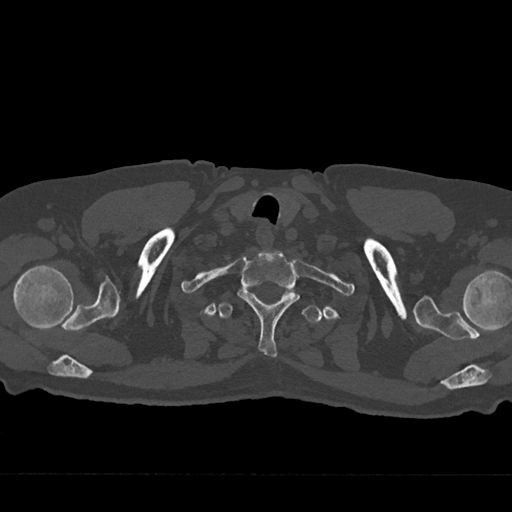
CT including the spine, one axial slice. Slice 651 of 797 in the series (ordered by position). Reconstruction kernel Br40s/3. Bone window (W 1800 / L 400 HU). 0.5 mm slice thickness. 512 × 512 image matrix, field of view 377 × 377 mm. Patient: male, 75 years. Case-level facts recorded for this patient, not image findings: primary cancer: renal; vertebrae with lytic lesions (as recorded): T4.
Outlined on this slice (semi-automatic segmentation, software-assisted and operator-edited):
- T1 vertebra: bounding box [x1, y1, x2, y2] px = [238, 250, 299, 357]
- T2 vertebra: [218, 289, 322, 323]